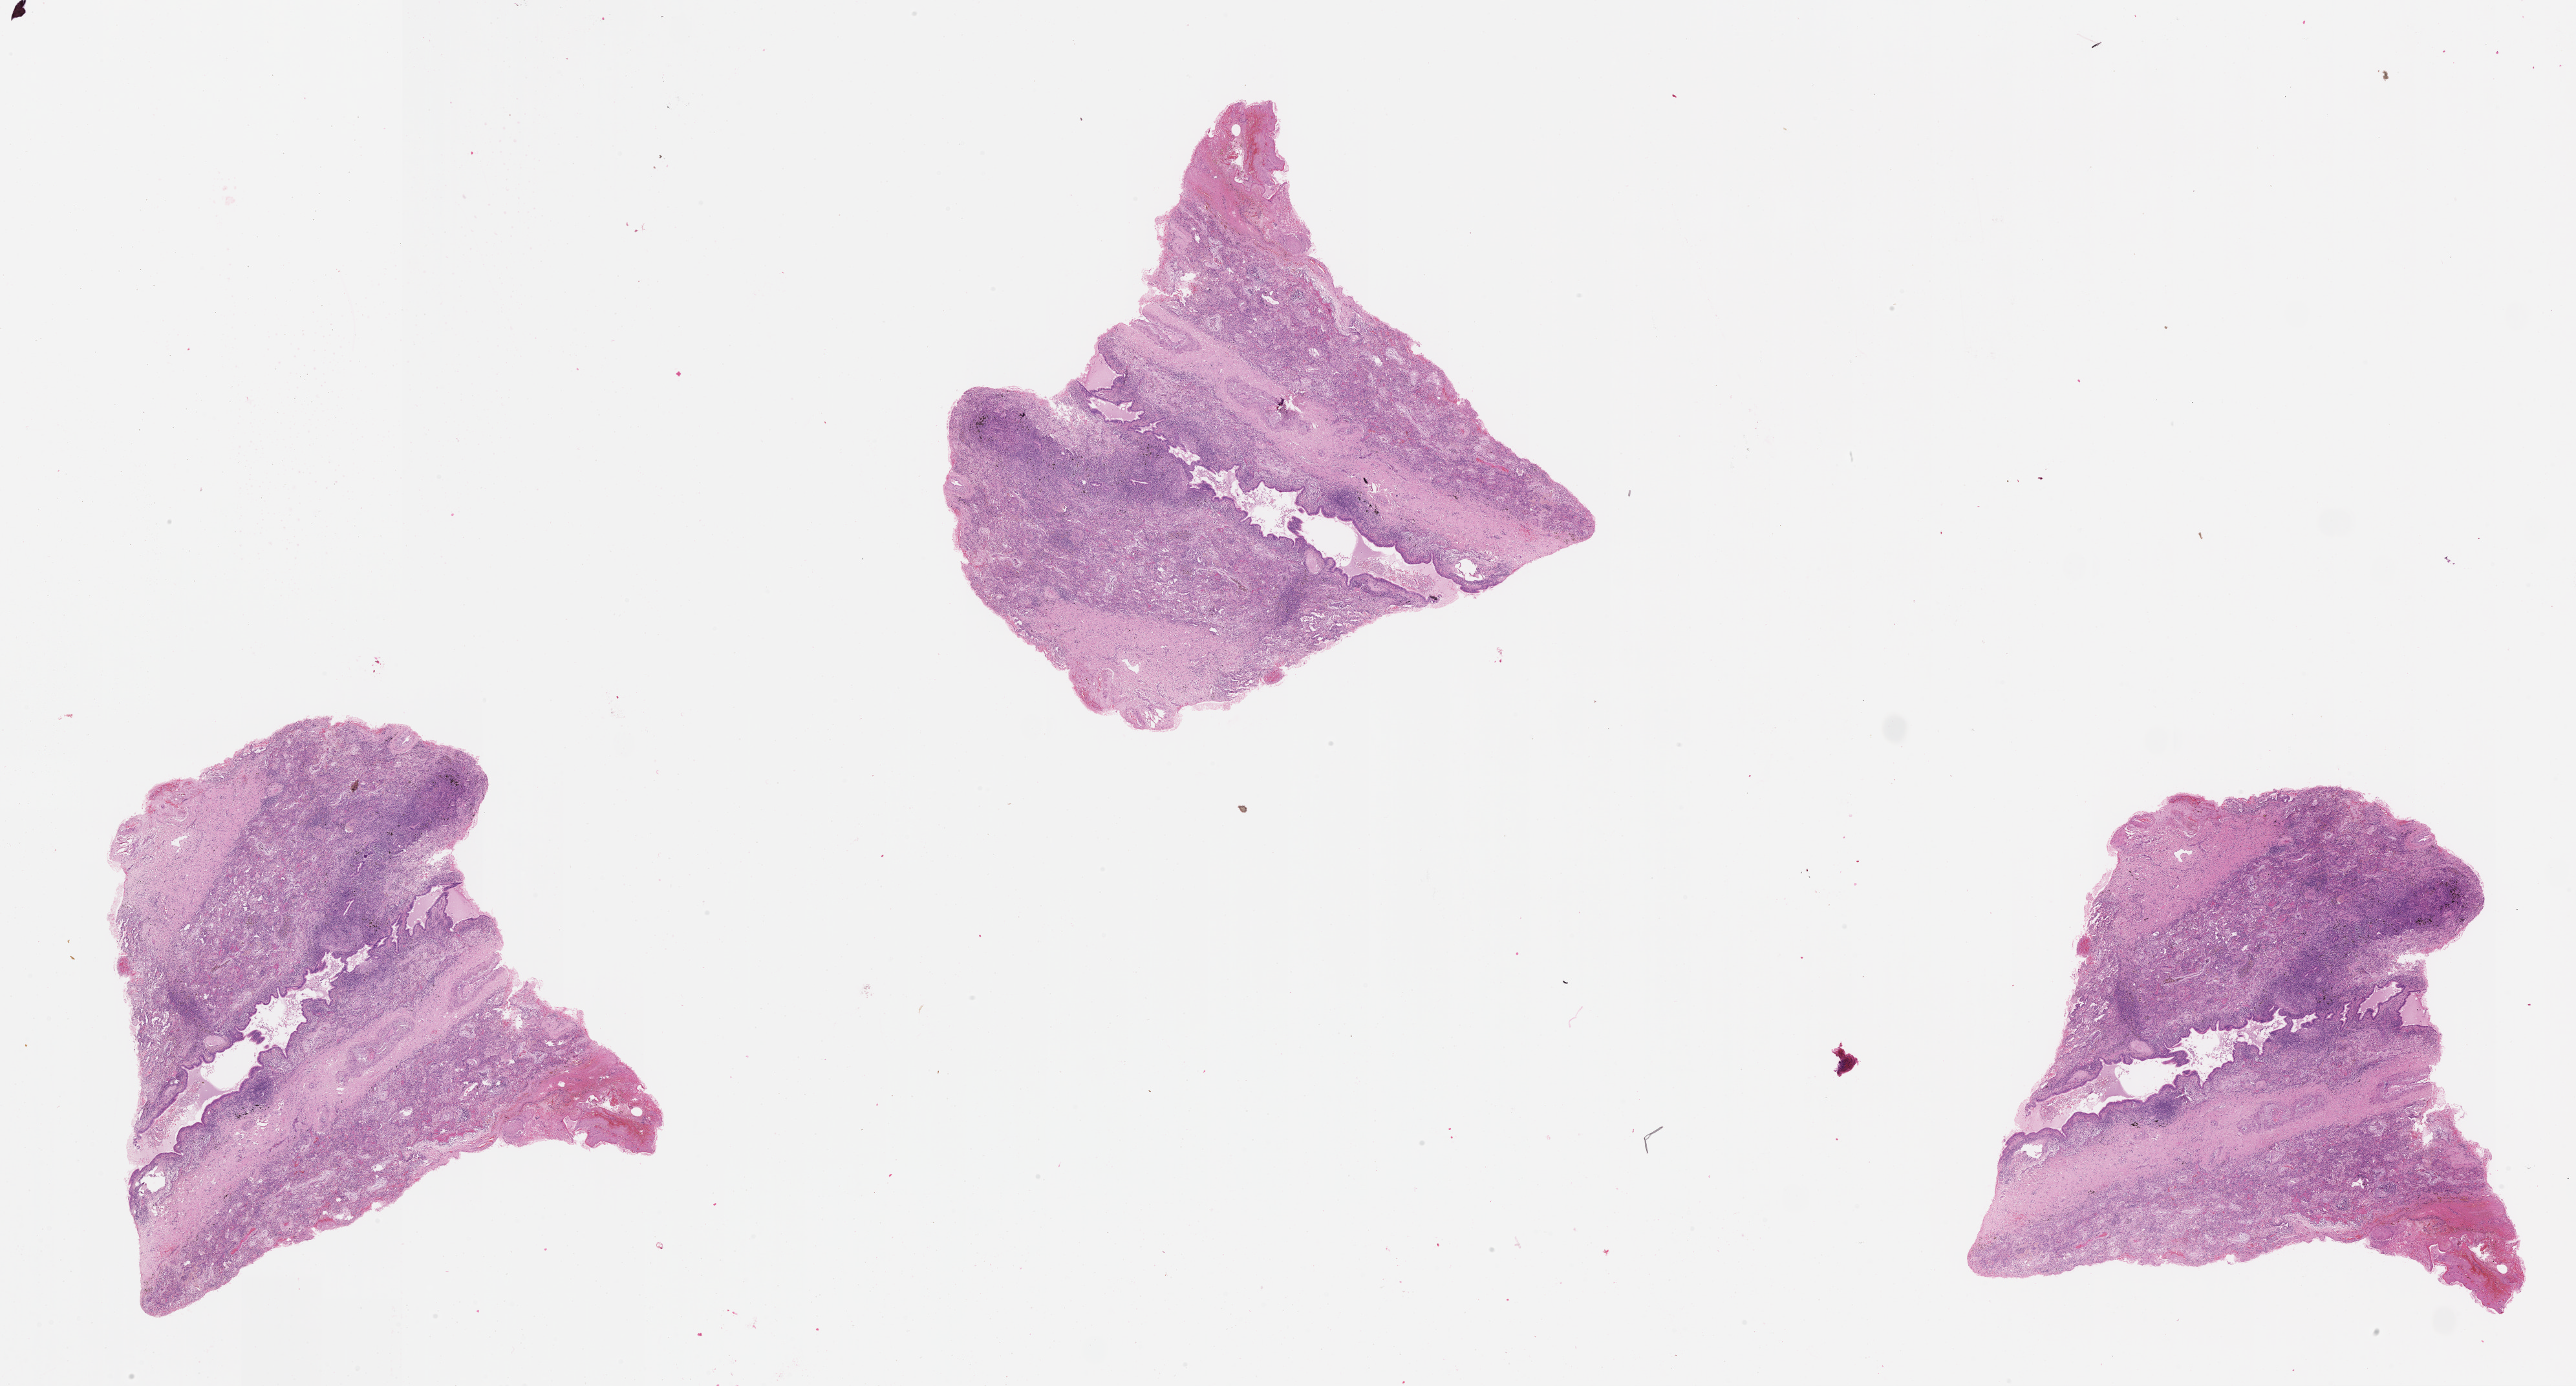
H&E-stained whole-slide image, a low-resolution overview of the entire scanned area, about 32.1 x 17.3 mm (from a 20x scan). Lung, normal (non-tumour) tissue. Patient: male, age 59 years.
* this section: normal (non-tumour) tissue from the same patient
* patient diagnosis (cohort enrolment): squamous cell carcinoma (lung)